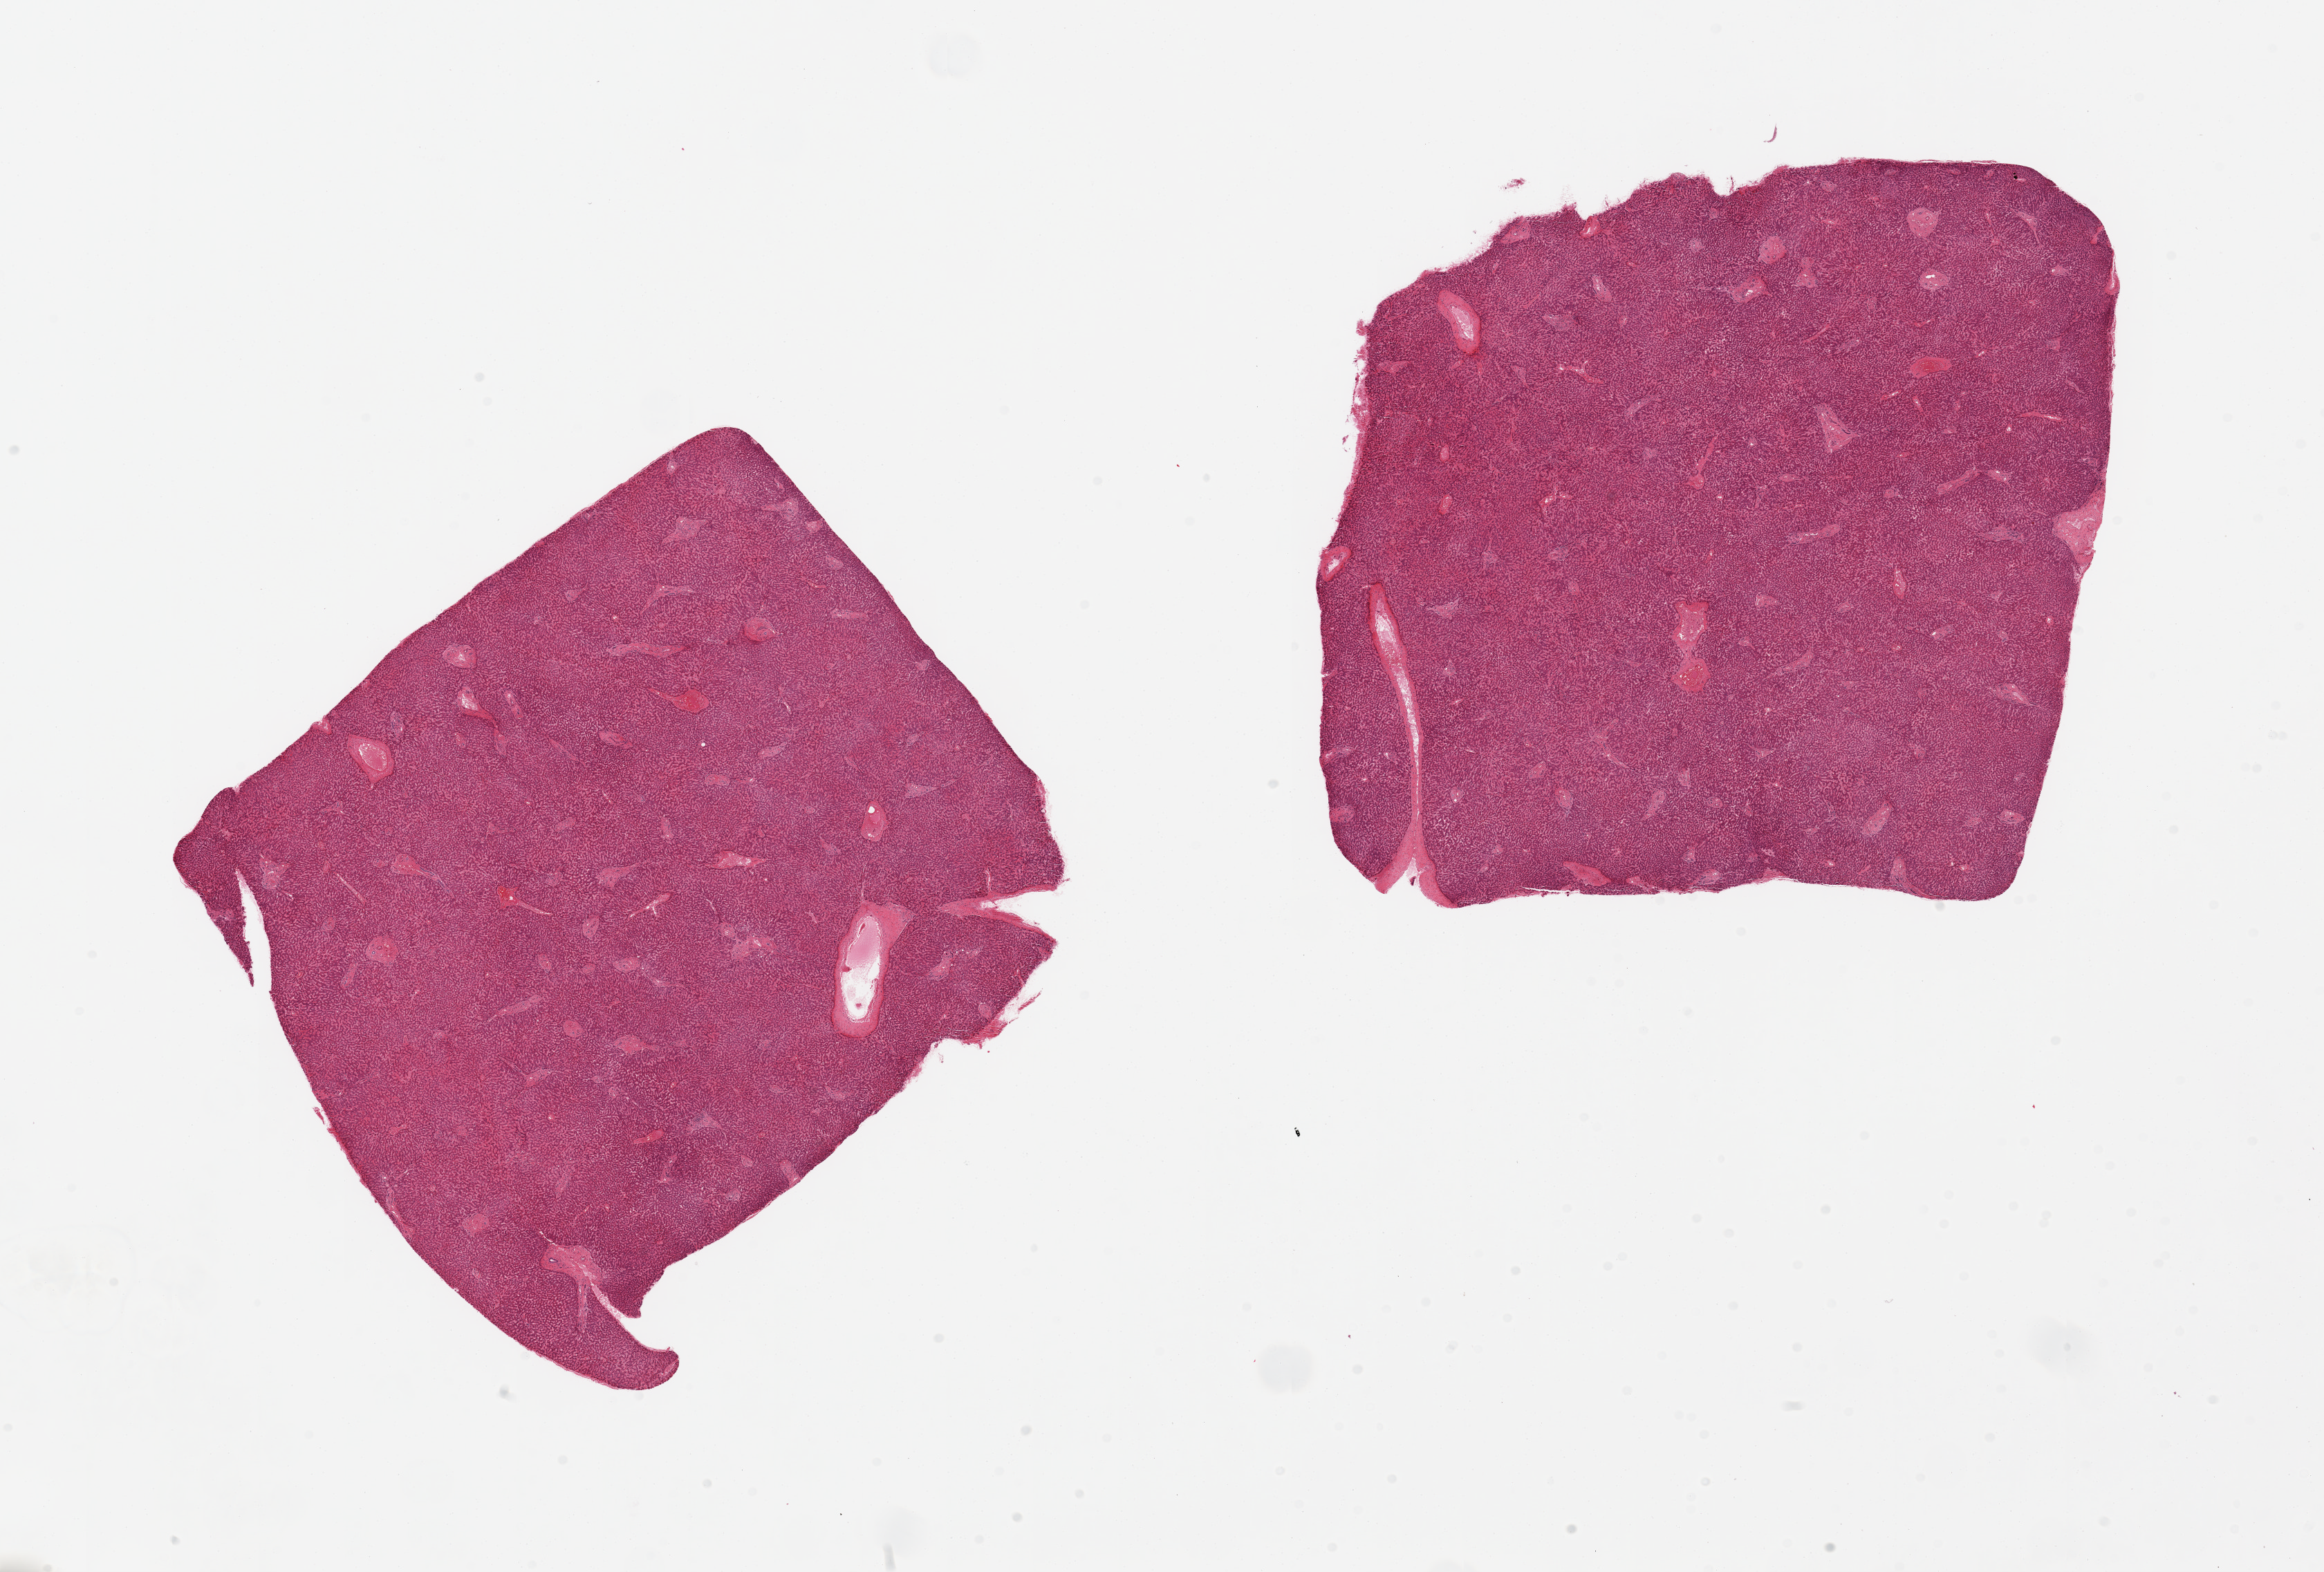
Digitized H&E-stained section — low-resolution overview of the scanned area, about 26.6 x 18.0 mm, PAXgene-fixed, paraffin-embedded tissue, target tissue: liver, tissue donor sample. Male donor.
Pathologist's review note for this sample: 2 pieces, minimal steatosis.